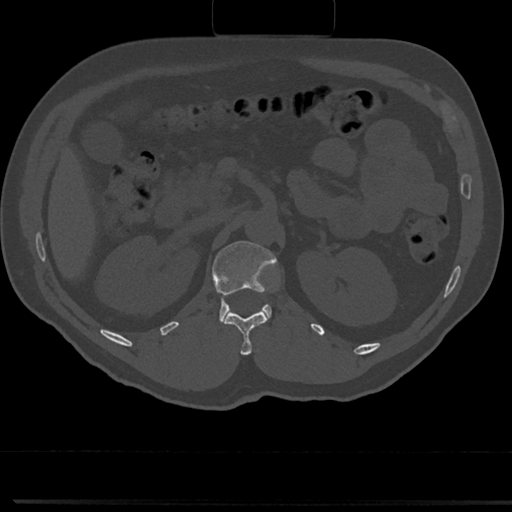
CT including the spine, one axial slice; position 111 of 817 along the scan axis; bone window (W 1800 / L 400 HU); 0.5 mm slice thickness; 512 × 512 image matrix. Patient: male, 61 years. From the clinical record (not read from this slice): primary cancer: prostate.
Outlined on this slice (semi-automatically segmented with operator editing):
- L1 vertebra: box from (x=213, y=240) to (x=278, y=326) px
- T12 vertebra: (x=223, y=311)–(x=268, y=354)